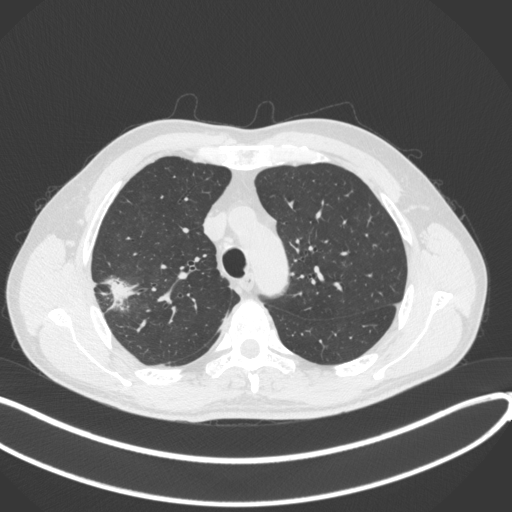
Chest CT, one axial slice. Position 313 of 381 along the scan axis. 120 kVp. Lung window (W 1500 / L -600 HU). 1 mm slice thickness. 512 × 512 image matrix, field of view 400 × 400 mm. Male patient, age 62 years. Case-level facts recorded for this patient, not image findings: clinical TNM (as recorded): T1c N0 M0.
Annotated regions visible in this slice (rectangle marked by the reading radiologist):
- lung tumour (recorded histology: adenocarcinoma): box from (x=99, y=270) to (x=136, y=315) px